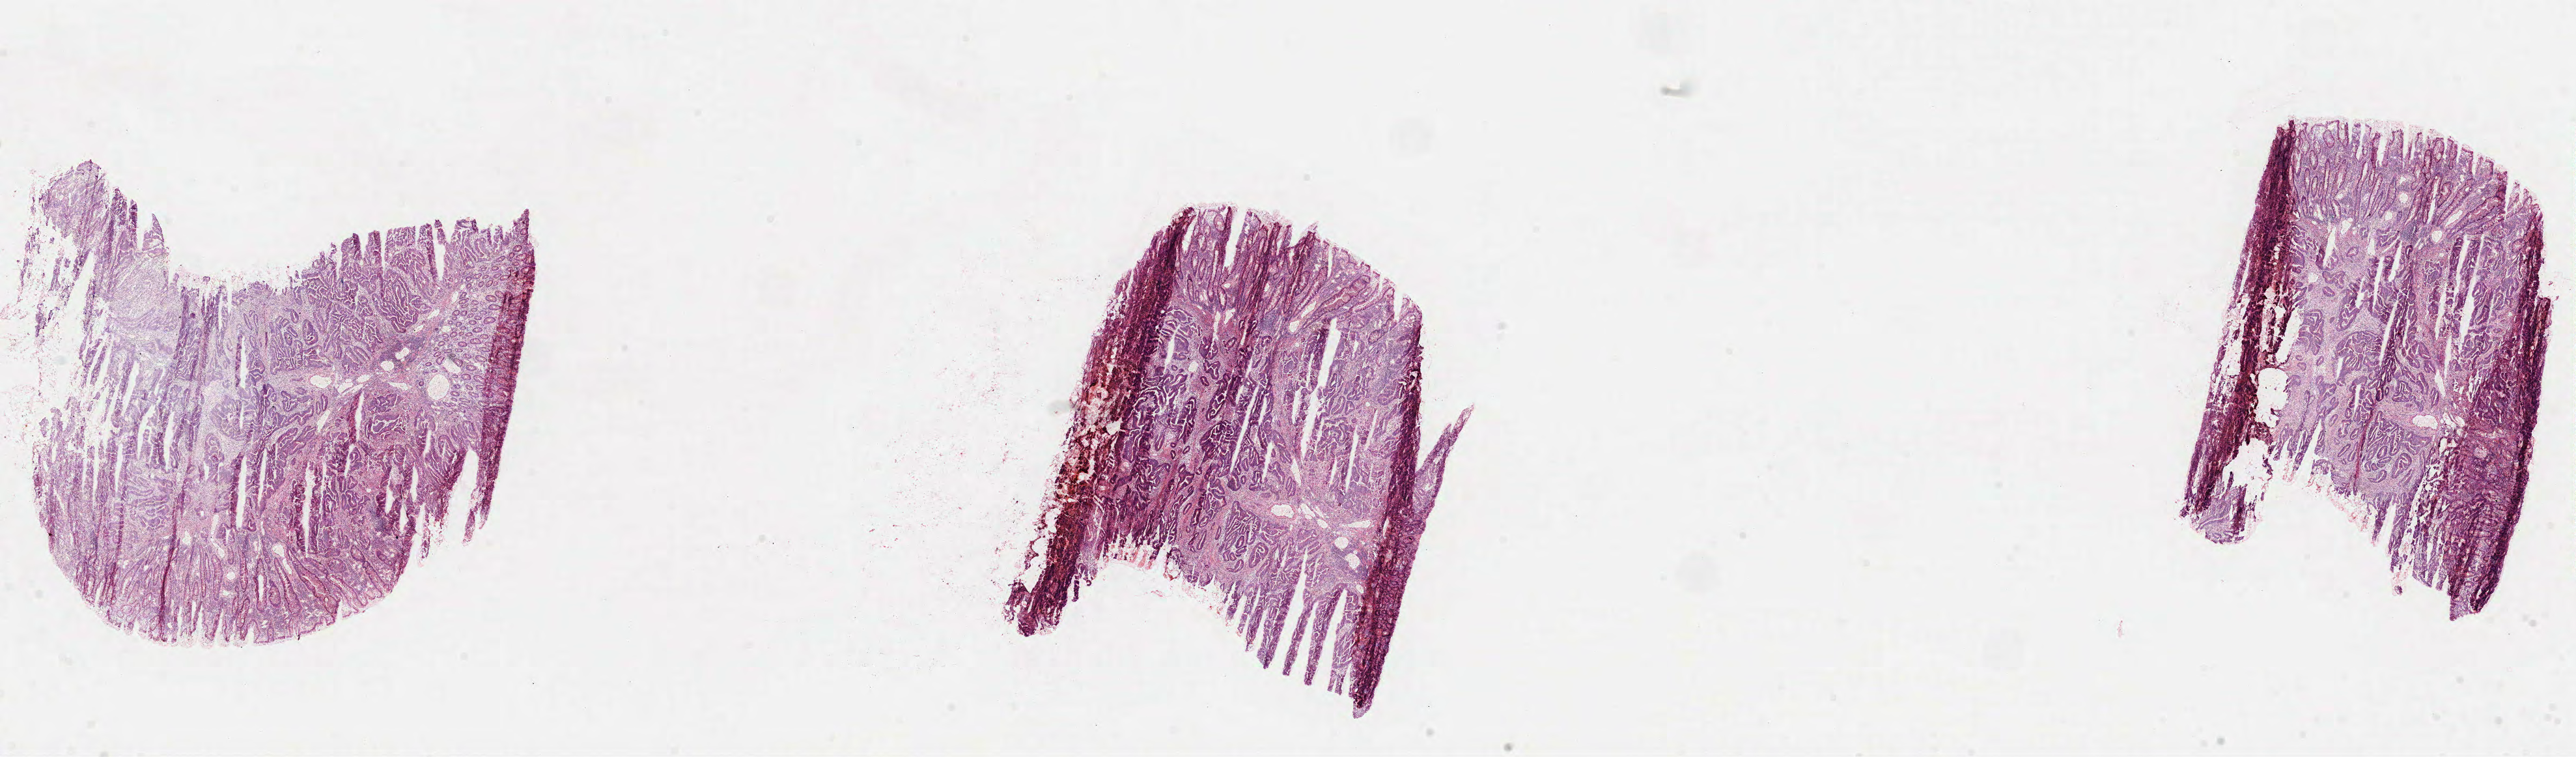
Whole-slide histology image, H&E — shown as a low-resolution overview of the whole scanned area (about 31.9 x 9.4 mm); formalin-fixed paraffin-embedded (FFPE) diagnostic section; rectum, primary tumour sample. Male patient; age at initial diagnosis 71 years.
AJCC pathologic stage: IIIA (7th edition). Pathologic diagnosis: Tubular adenocarcinoma. TNM: T3 N1 M0. Lymph nodes positive (case pathology): 3 of 8 examined.